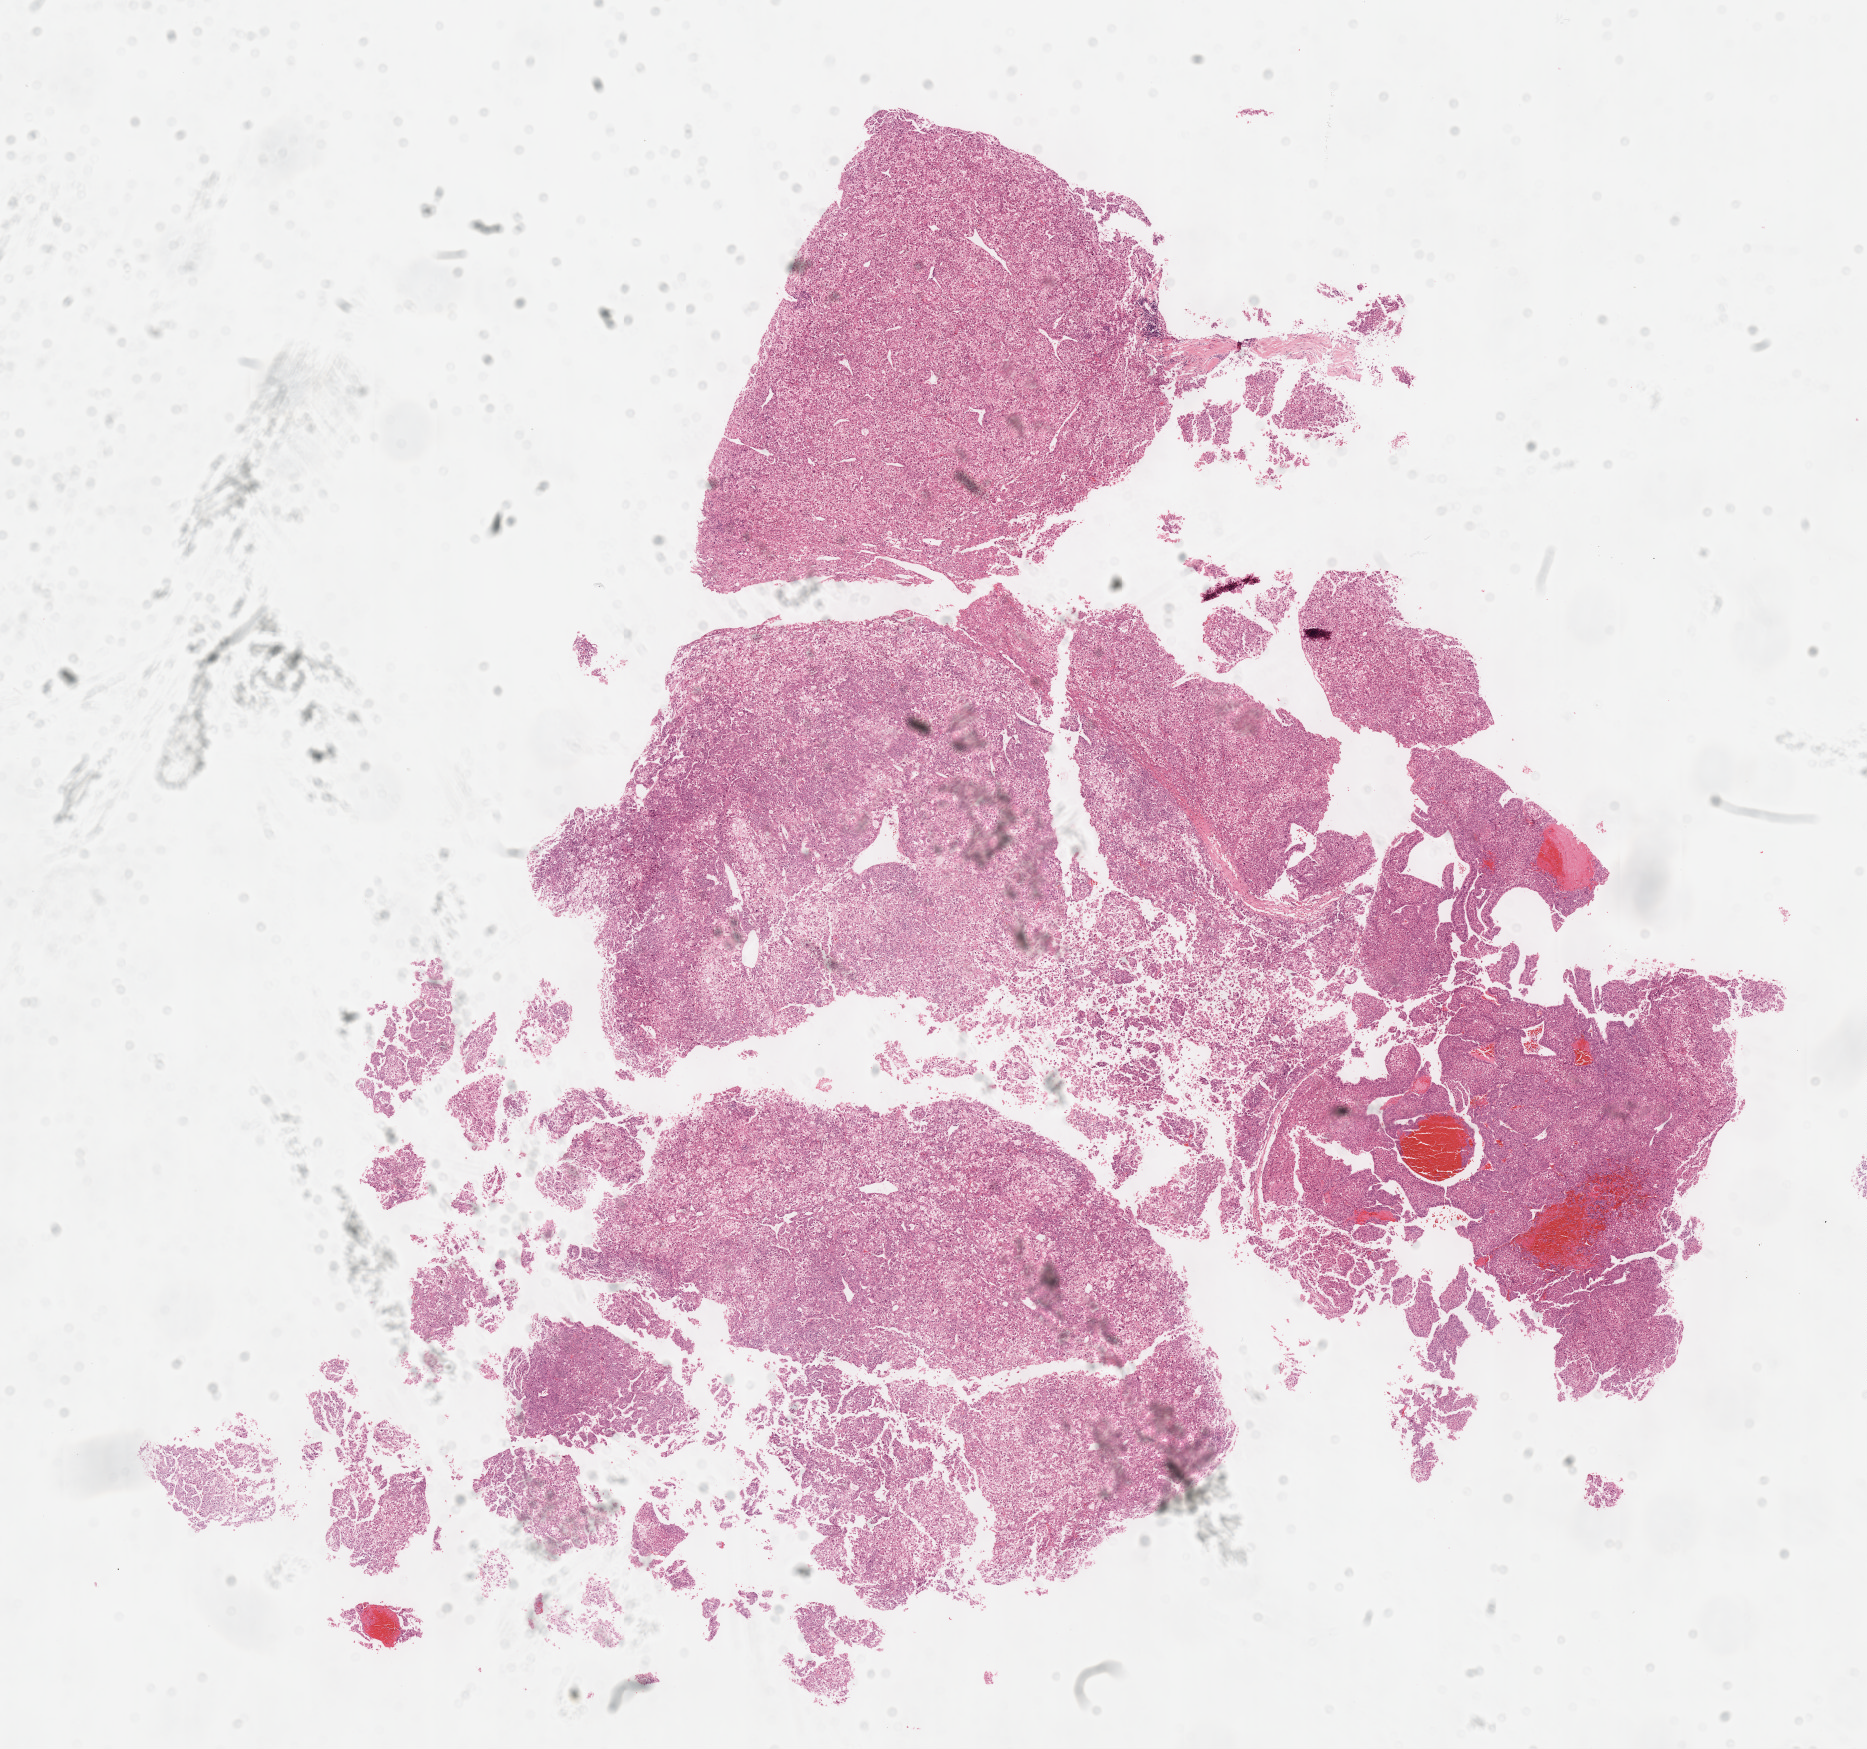
H&E whole-slide image — low-resolution overview of the scanned area, about 15.1 x 14.1 mm, formalin-fixed paraffin-embedded (FFPE) diagnostic section, primary tumour sample from the liver. Female, age 66 years at initial diagnosis. Histologic grade: G3 (poorly differentiated).
Pathologic diagnosis: Hepatocellular carcinoma, NOS. AJCC pathologic stage: I.